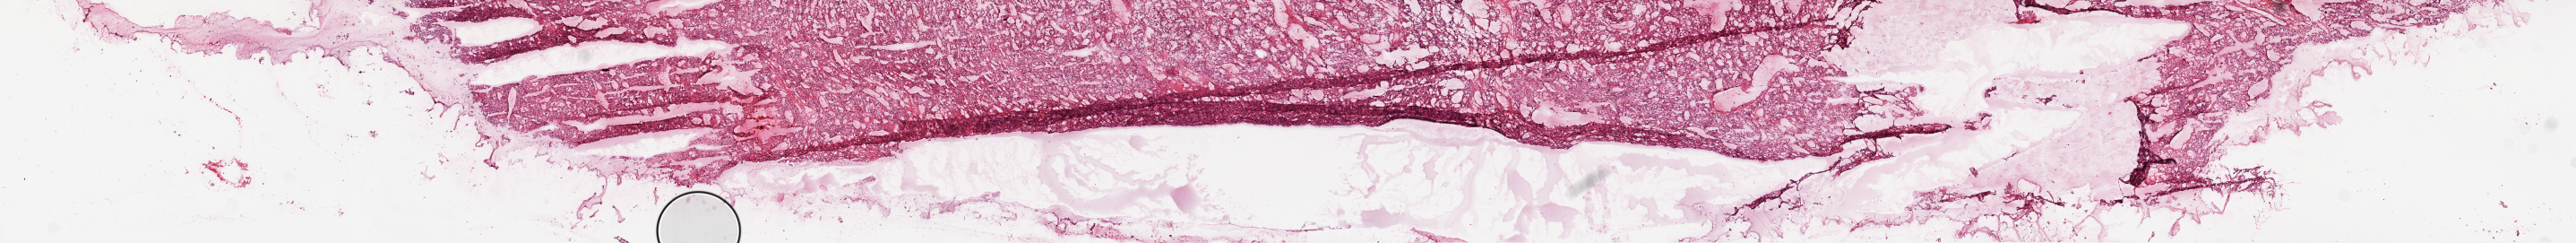
Whole-slide histology image, H&E, whole scanned area (about 23.1 x 2.2 mm) shown as a low-resolution overview, frozen section from the top of the tissue portion, sample: primary tumour, kidney. Female patient; age at initial diagnosis 80 years. Histologic grade: G2 (moderately differentiated). Composition of this section per pathologist review: tumour cells 95%, tumour nuclei 90%, normal cells 0%, stromal cells 5%, necrosis 0%.
* laterality: left
* TNM: T1b N0 M0
* pathologic diagnosis: Clear cell adenocarcinoma, NOS
* AJCC pathologic stage: I